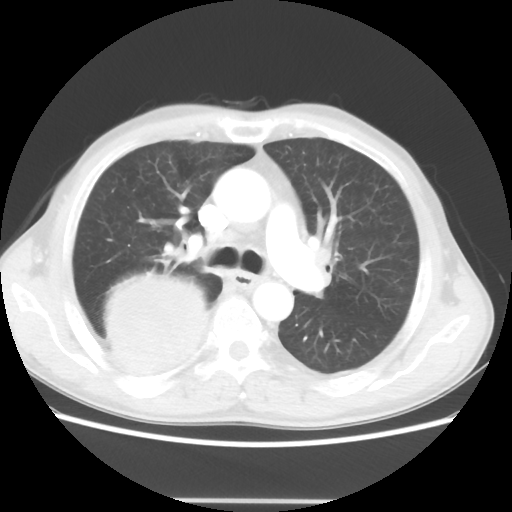
Chest CT, one axial slice; position 31 of 48 along the scan axis; reconstruction kernel STANDARD; 100 kVp; lung window (W 1500 / L -600 HU); 5 mm slice thickness; 512 × 512 image matrix, field of view 361 × 361 mm. Patient: male, 66 years. From the clinical record (not read from this slice): clinical TNM (as recorded): T4 N1 M1.
Structures marked on this image (rectangle marked by the reading radiologist):
- lung tumour (recorded histology: small cell carcinoma): bounding box (x1, y1, x2, y2) in pixels: (104, 265, 210, 369)